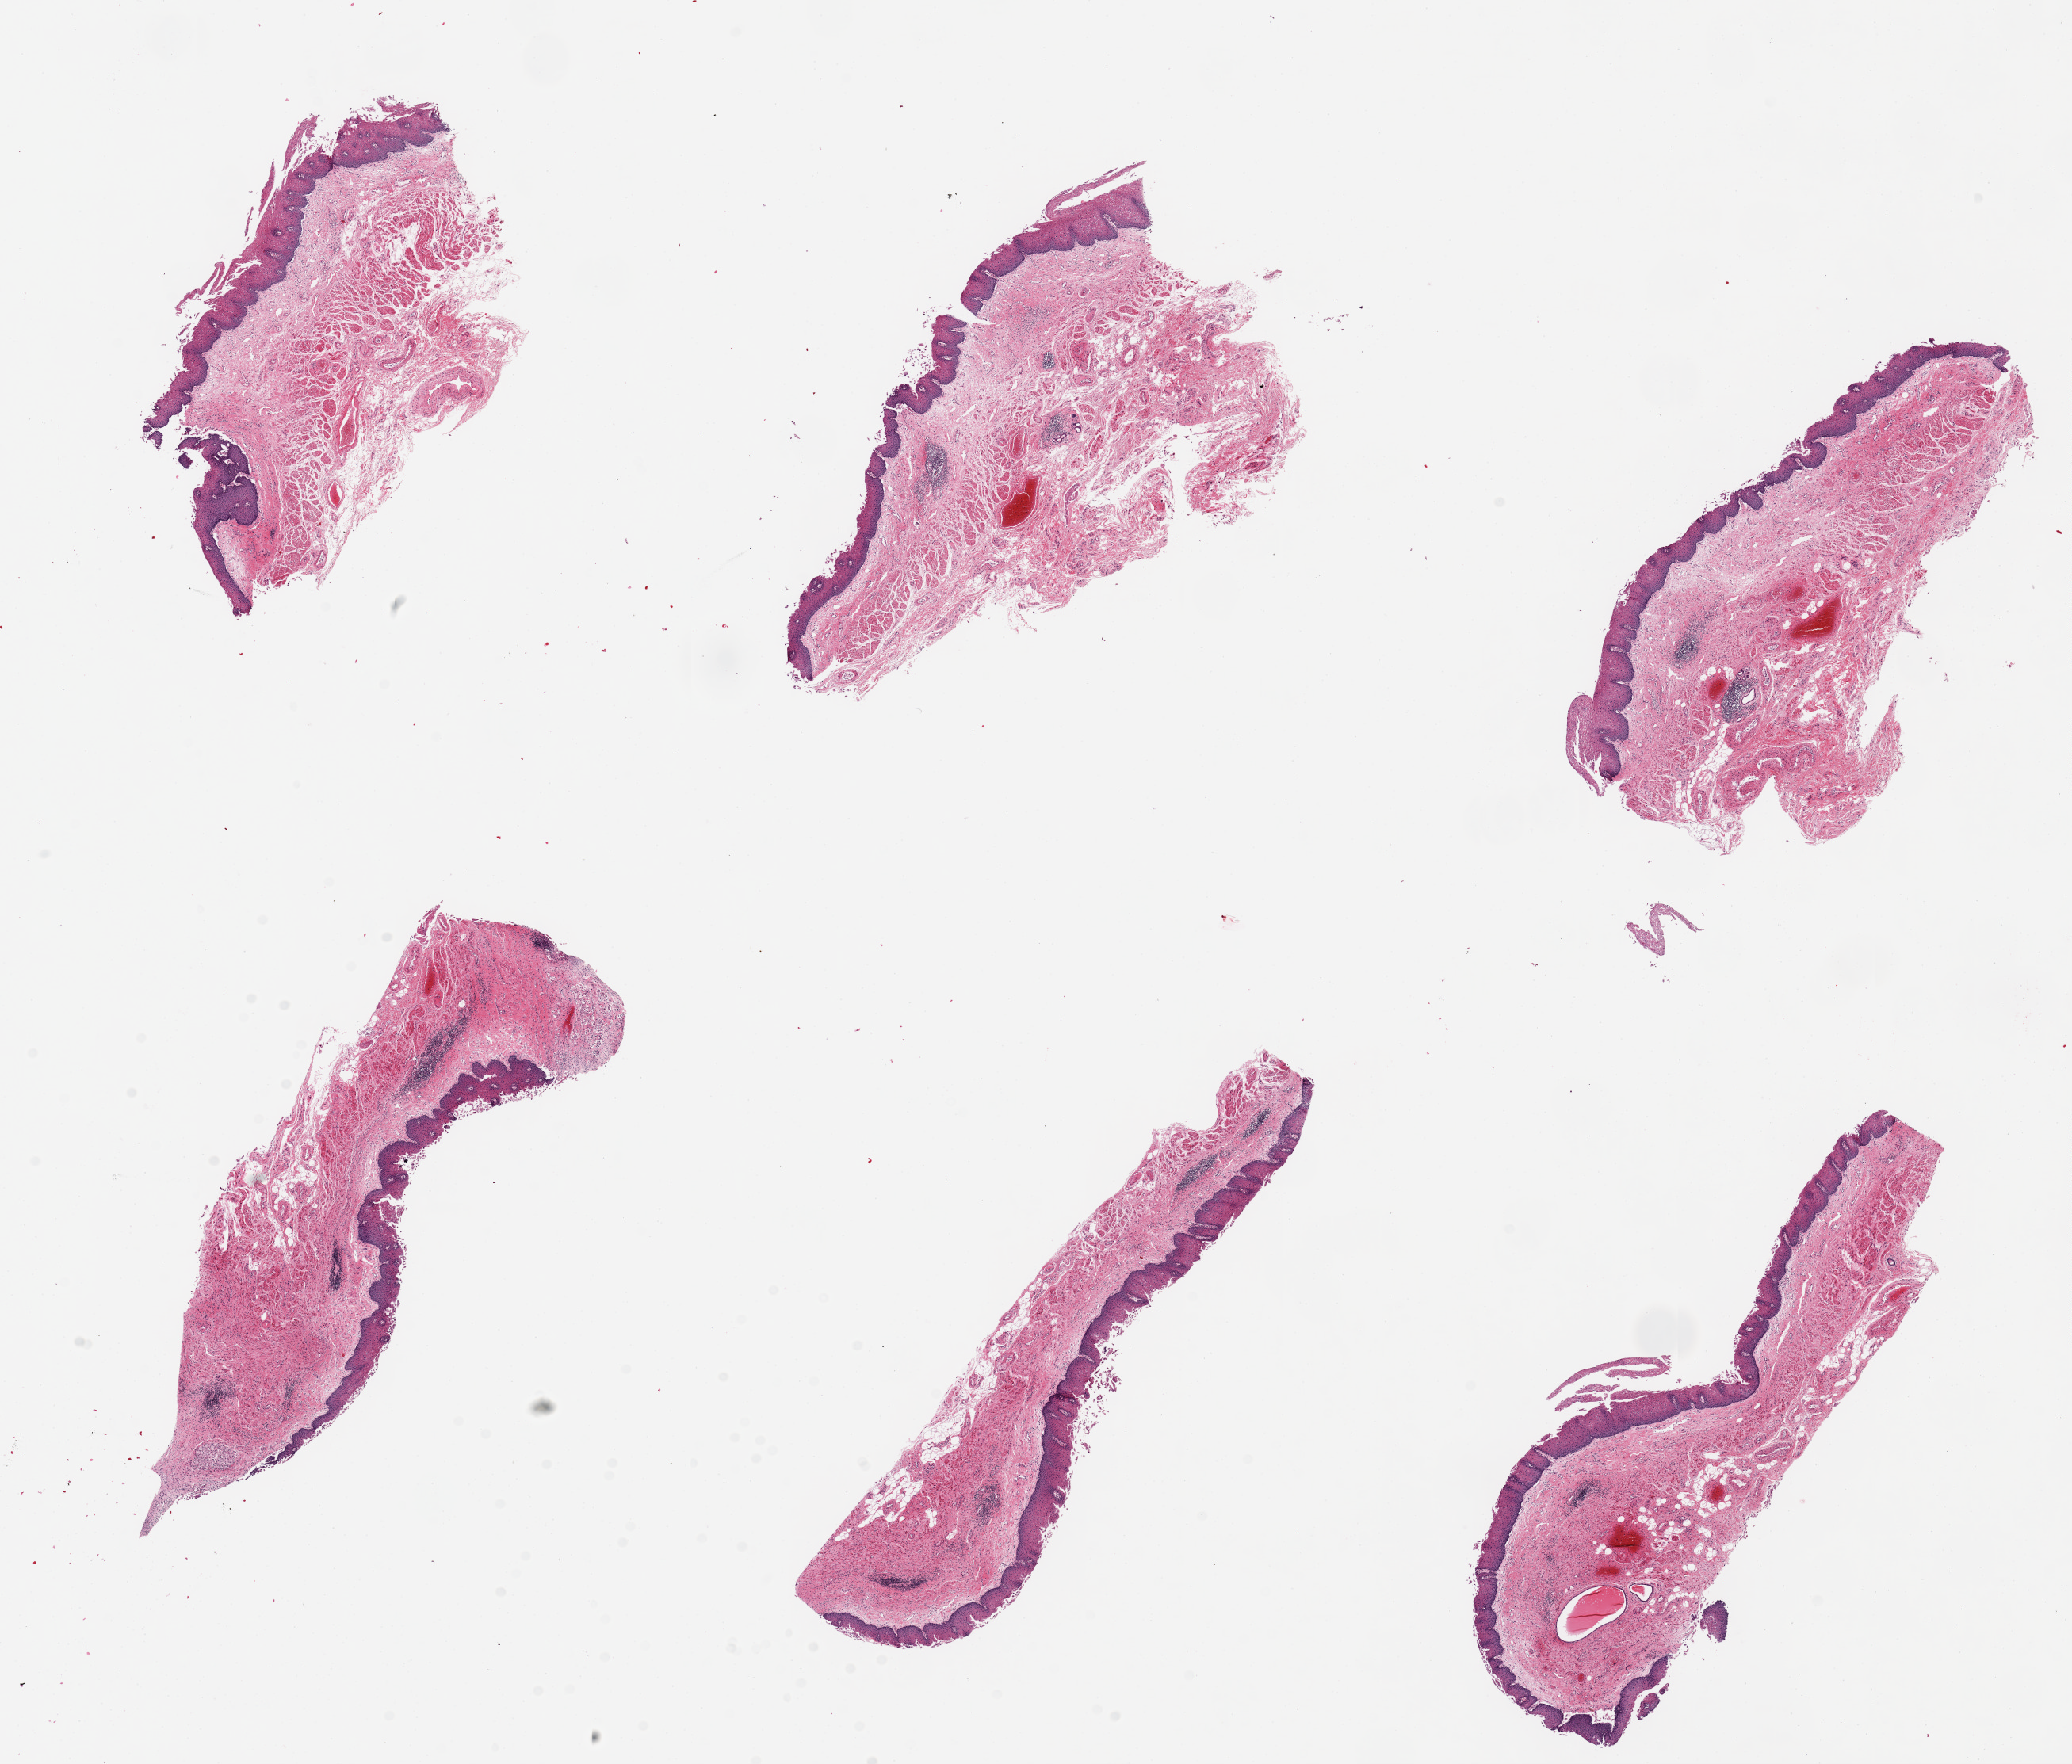
Digitized hematoxylin and eosin (H&E)-stained section — a low-resolution overview of the entire scanned area, about 20.7 x 17.6 mm. PAXgene-fixed, paraffin-embedded tissue. Sampled site (target tissue): esophageal mucous membrane. Tissue donor sample. Male donor.
Pathologist's review note for this sample: 6 pieces, up to 7x3mm.